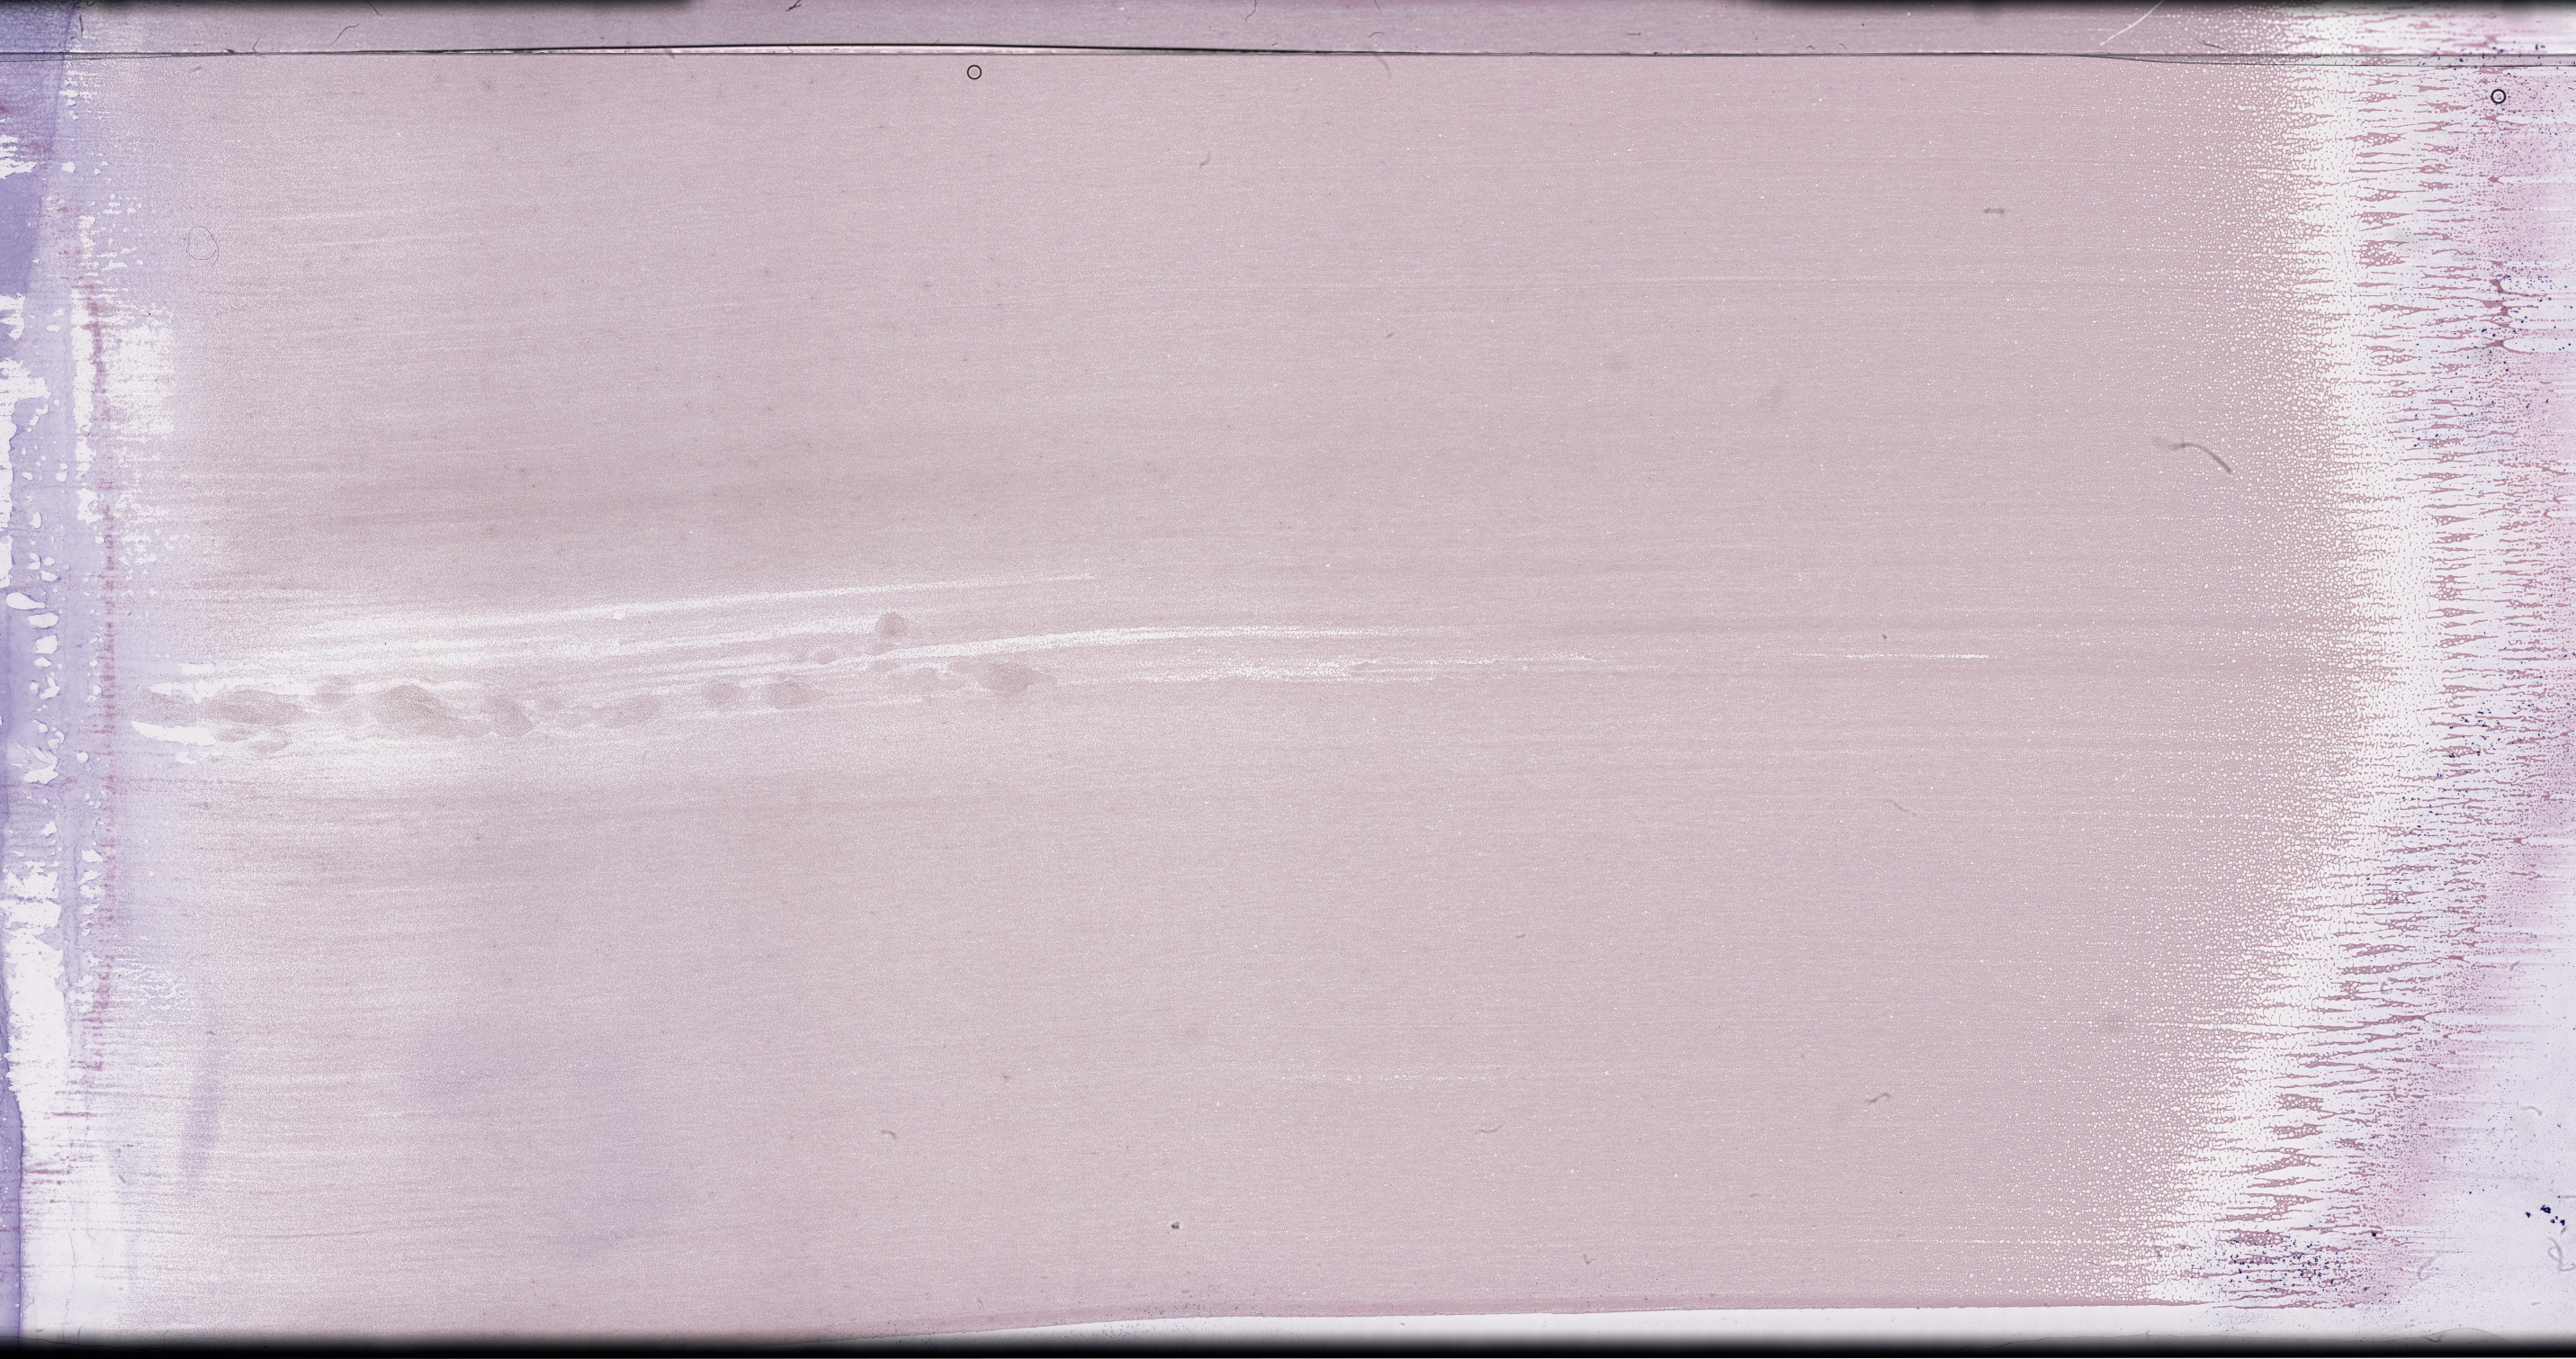
Whole-slide image of a whole blood smear, Wright–Giemsa stain, shown as a low-resolution overview of the whole scanned area (about 46.2 x 24.4 mm); specimen time point: collected on treatment. Patient sex: female.
From a patient with: Plasma Cell Myeloma.